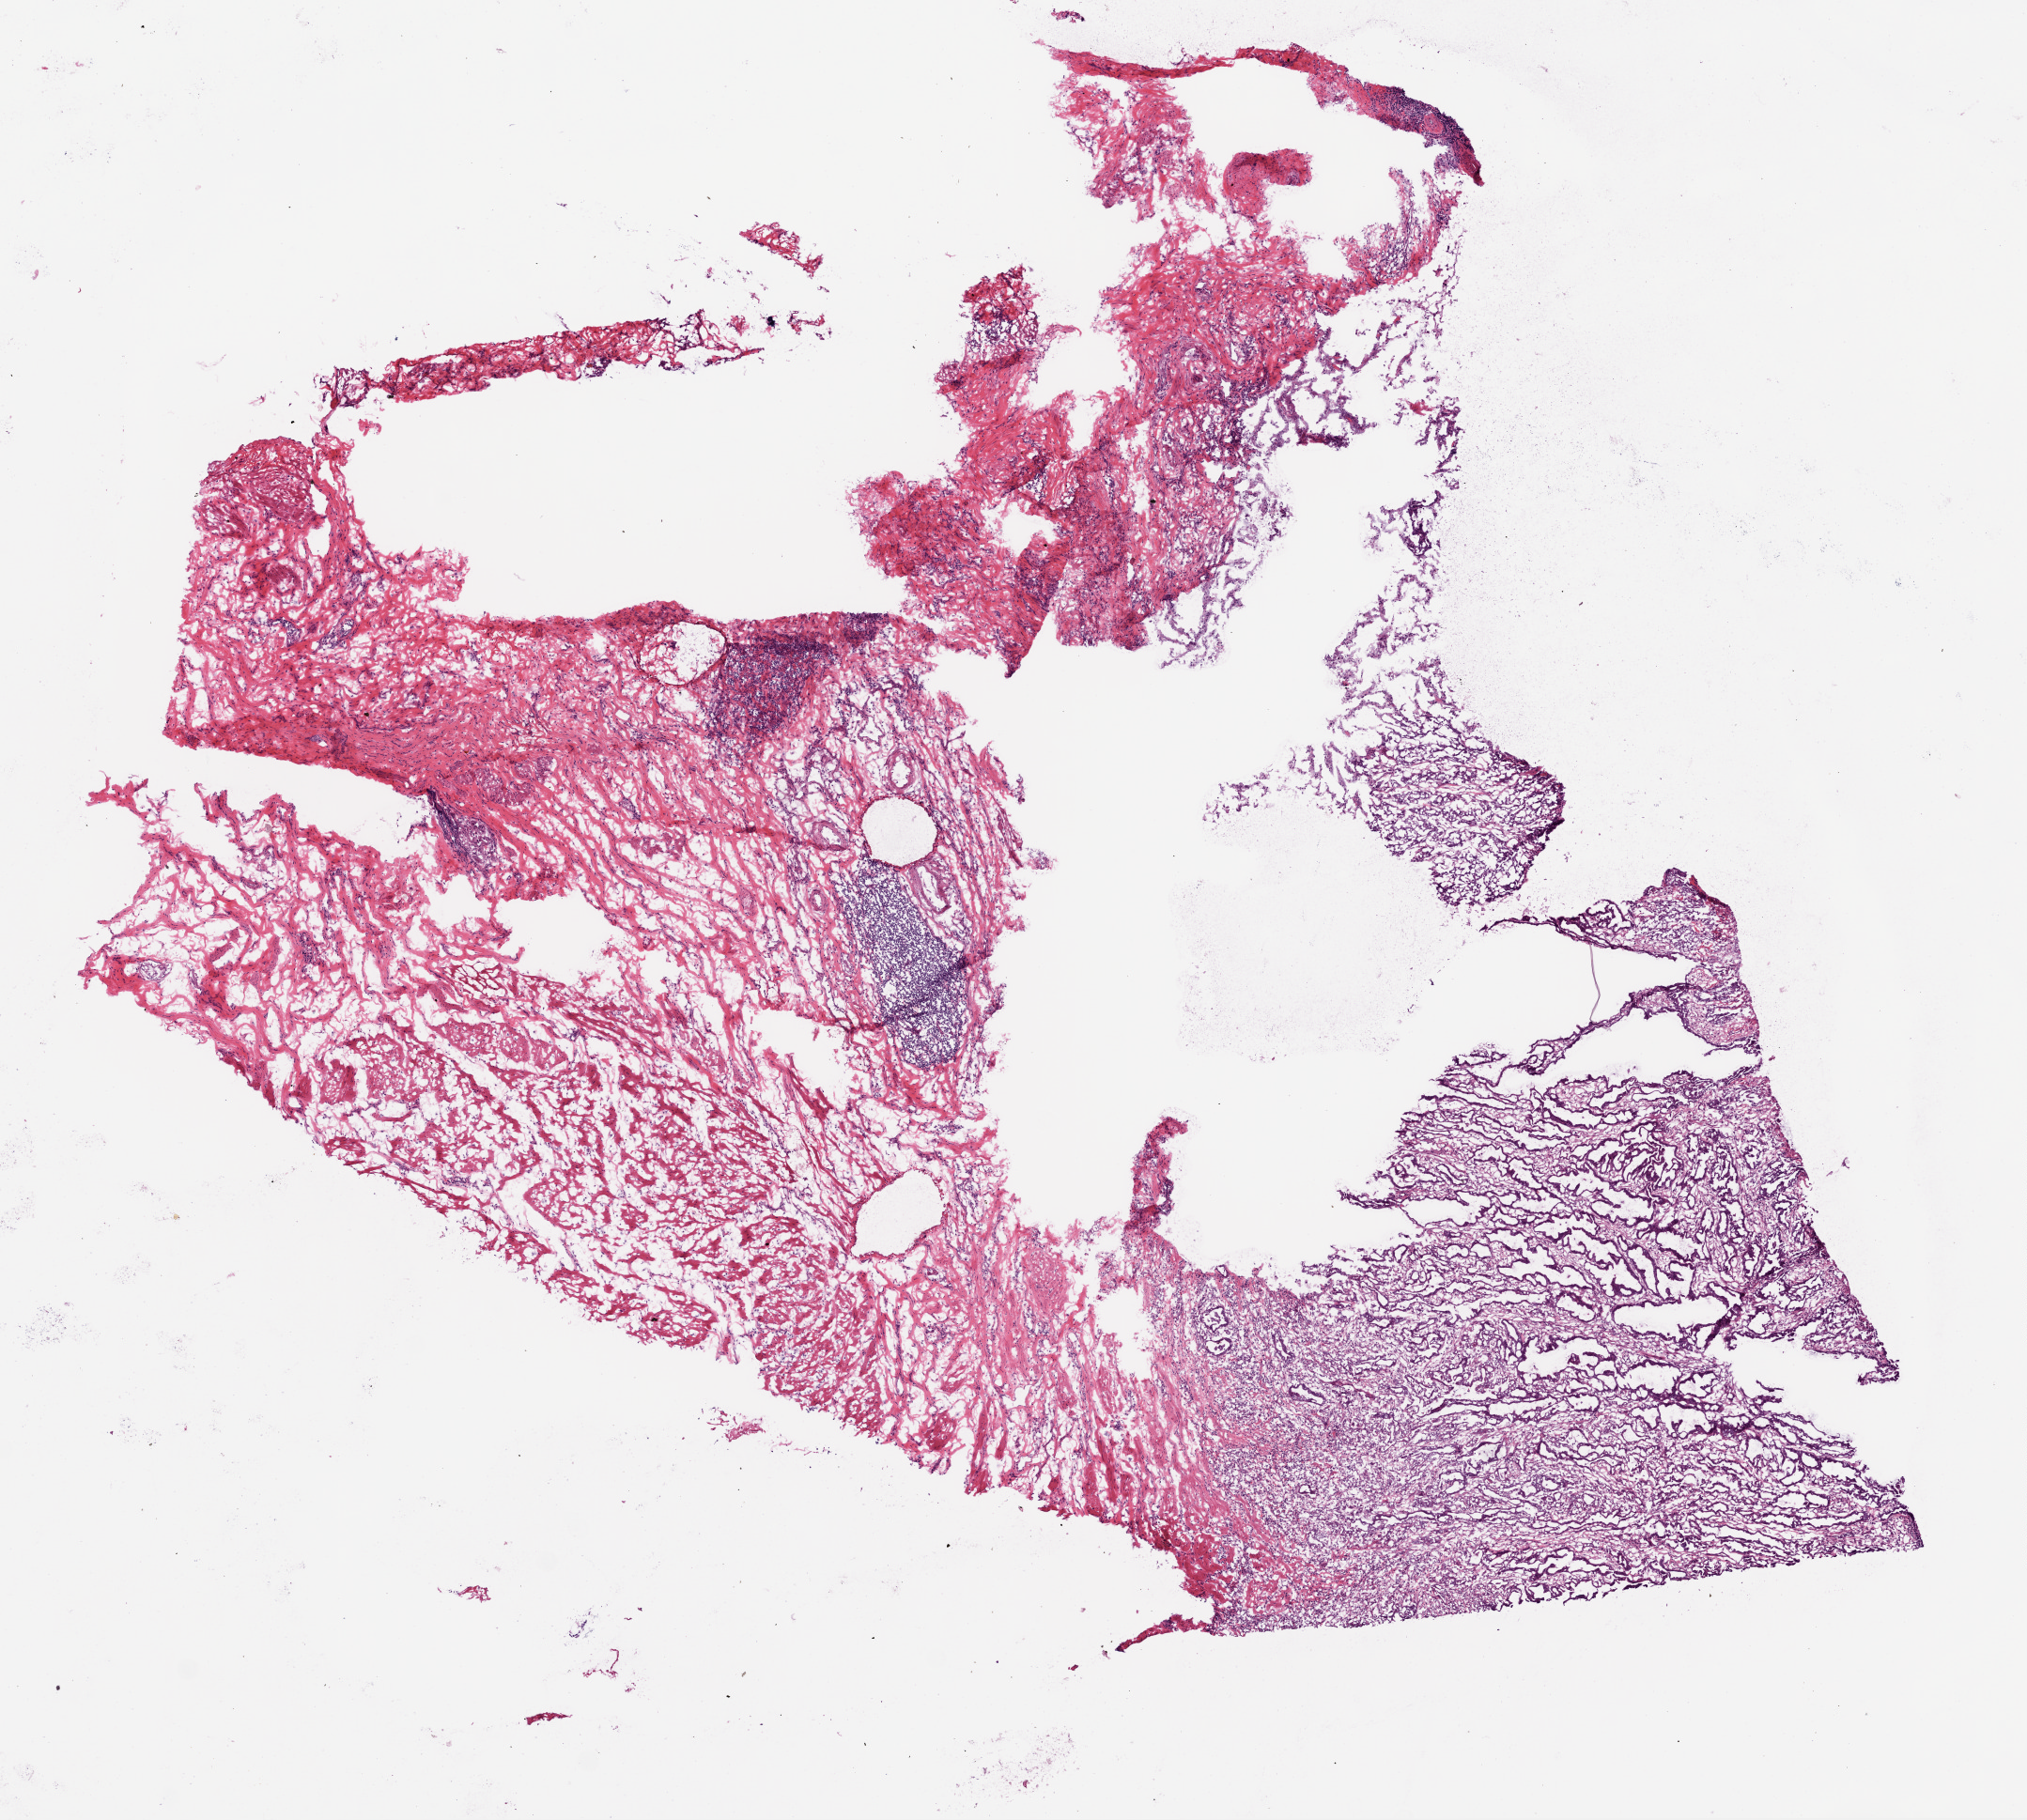
Hematoxylin and eosin (H&E) stained whole-slide image — shown as a low-resolution overview of the whole scanned area (about 8.7 x 7.8 mm, acquisition: 20x scan). Frozen section from the top of the tissue portion. Sample: primary tumour, stomach. Patient: female, age at initial diagnosis 69 years. Histologic grade: G3 (poorly differentiated). Composition of this section per pathologist review: tumour cells 60%, tumour nuclei 60%, normal cells 0%, stromal cells 20%, necrosis 0%.
- lymph nodes positive (case pathology): 0 of 2 examined
- TNM: T2 N0 M0
- AJCC pathologic stage: IB
- pathologic diagnosis: Adenocarcinoma, NOS (body of stomach)